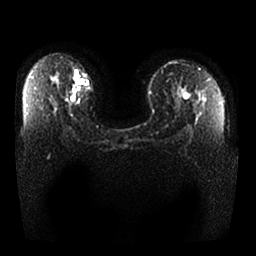
Breast MRI, one axial slice. Position 19 of 25 along the scan axis. Diffusion-weighted series; image 2 of 4 stored at this slice position (different b-values; order by instance number). 1.5 T. 256 × 256 image matrix, field of view 370 × 370 mm. Female patient.
Annotated regions visible in this slice (manually delineated by an expert):
- tumour on diffusion-weighted imaging: bounding box <76,78,84,85> (left, top, right, bottom; pixels)